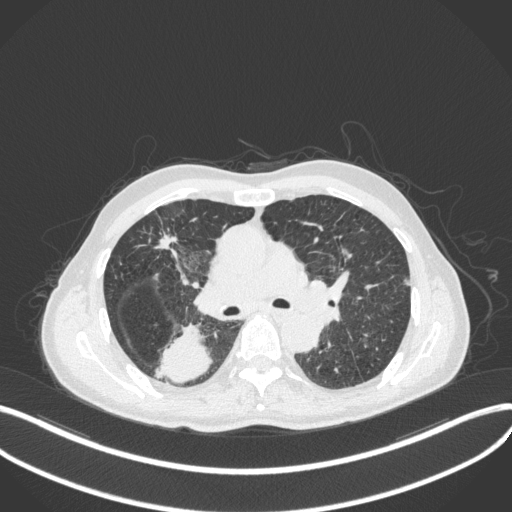
Chest CT, one axial slice; position 275 of 423 along the scan axis; reconstruction kernel B31f; 120 kVp; lung window (W 1500 / L -600 HU); 1 mm slice thickness; 512 × 512 image matrix, field of view 400 × 400 mm. Male patient, age 79 years. Case-level facts recorded for this patient, not image findings: clinical TNM (as recorded): T3 N0 M0.
Annotated regions visible in this slice (rectangle marked by the reading radiologist):
- lung tumour (recorded histology: adenocarcinoma): box from (x=149, y=319) to (x=213, y=385) px